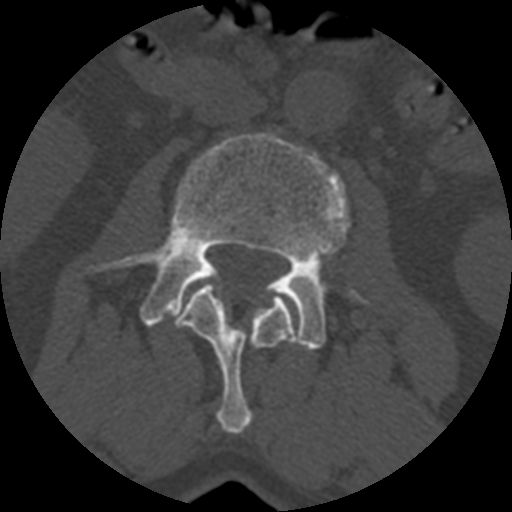
CT including the spine, one axial slice; position 317 of 399 along the scan axis; reconstruction kernel STANDARD; bone window (W 1800 / L 400 HU); 1.25 mm slice thickness; 512 × 512 image matrix, field of view 160 × 160 mm. Patient age 71 years. Case-level facts recorded for this patient, not image findings: primary cancer: prostate.
Annotated regions visible in this slice (semi-automatically segmented with operator editing):
- L2 vertebra: bounding box <174,284,295,434> (left, top, right, bottom; pixels)
- L3 vertebra: <86,131,368,350>